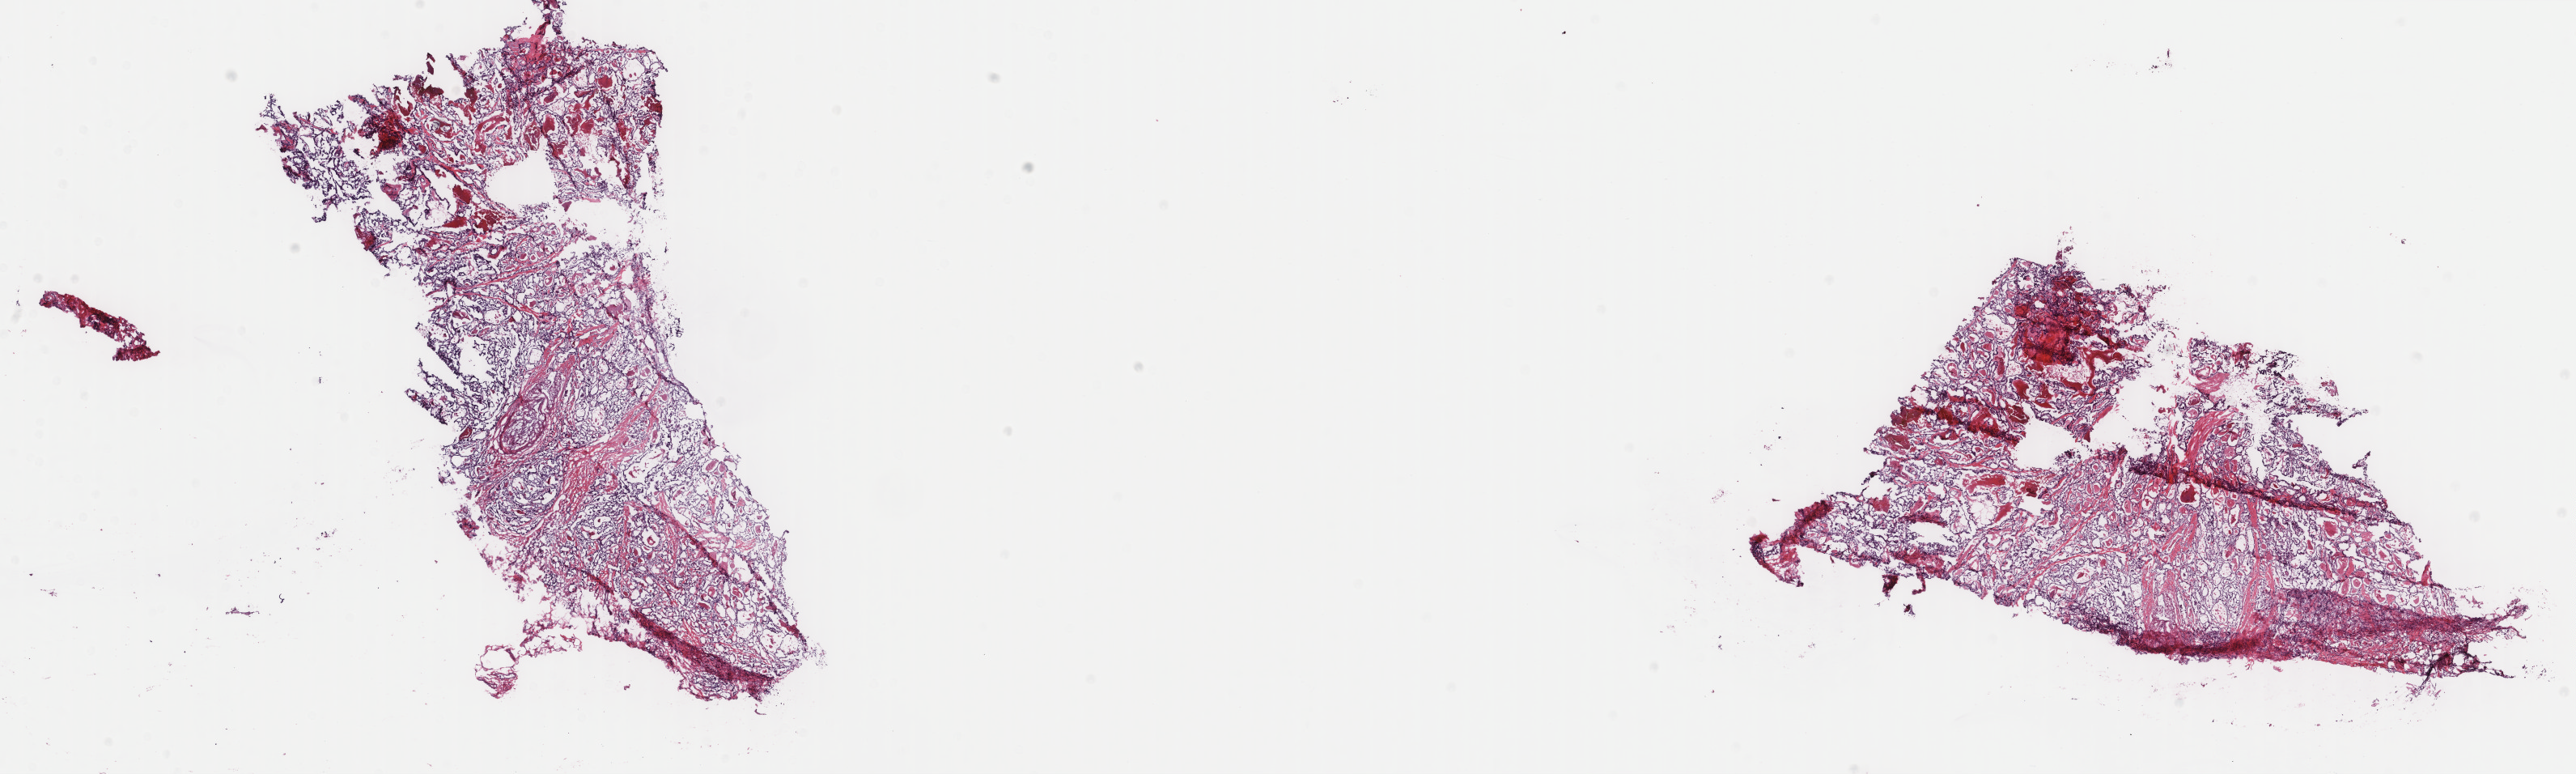
Digitized Hematoxylin and eosin (H&E) stained tissue section (whole slide) — low-resolution overview of the scanned area, about 25.3 x 7.6 mm, frozen section, thyroid, primary tumour sample. Male, age 77 years at initial diagnosis. Composition of this section per pathologist review: tumour cells 70%, tumour nuclei 70%.
Histologic diagnosis: Papillary adenocarcinoma, NOS (thyroid gland).